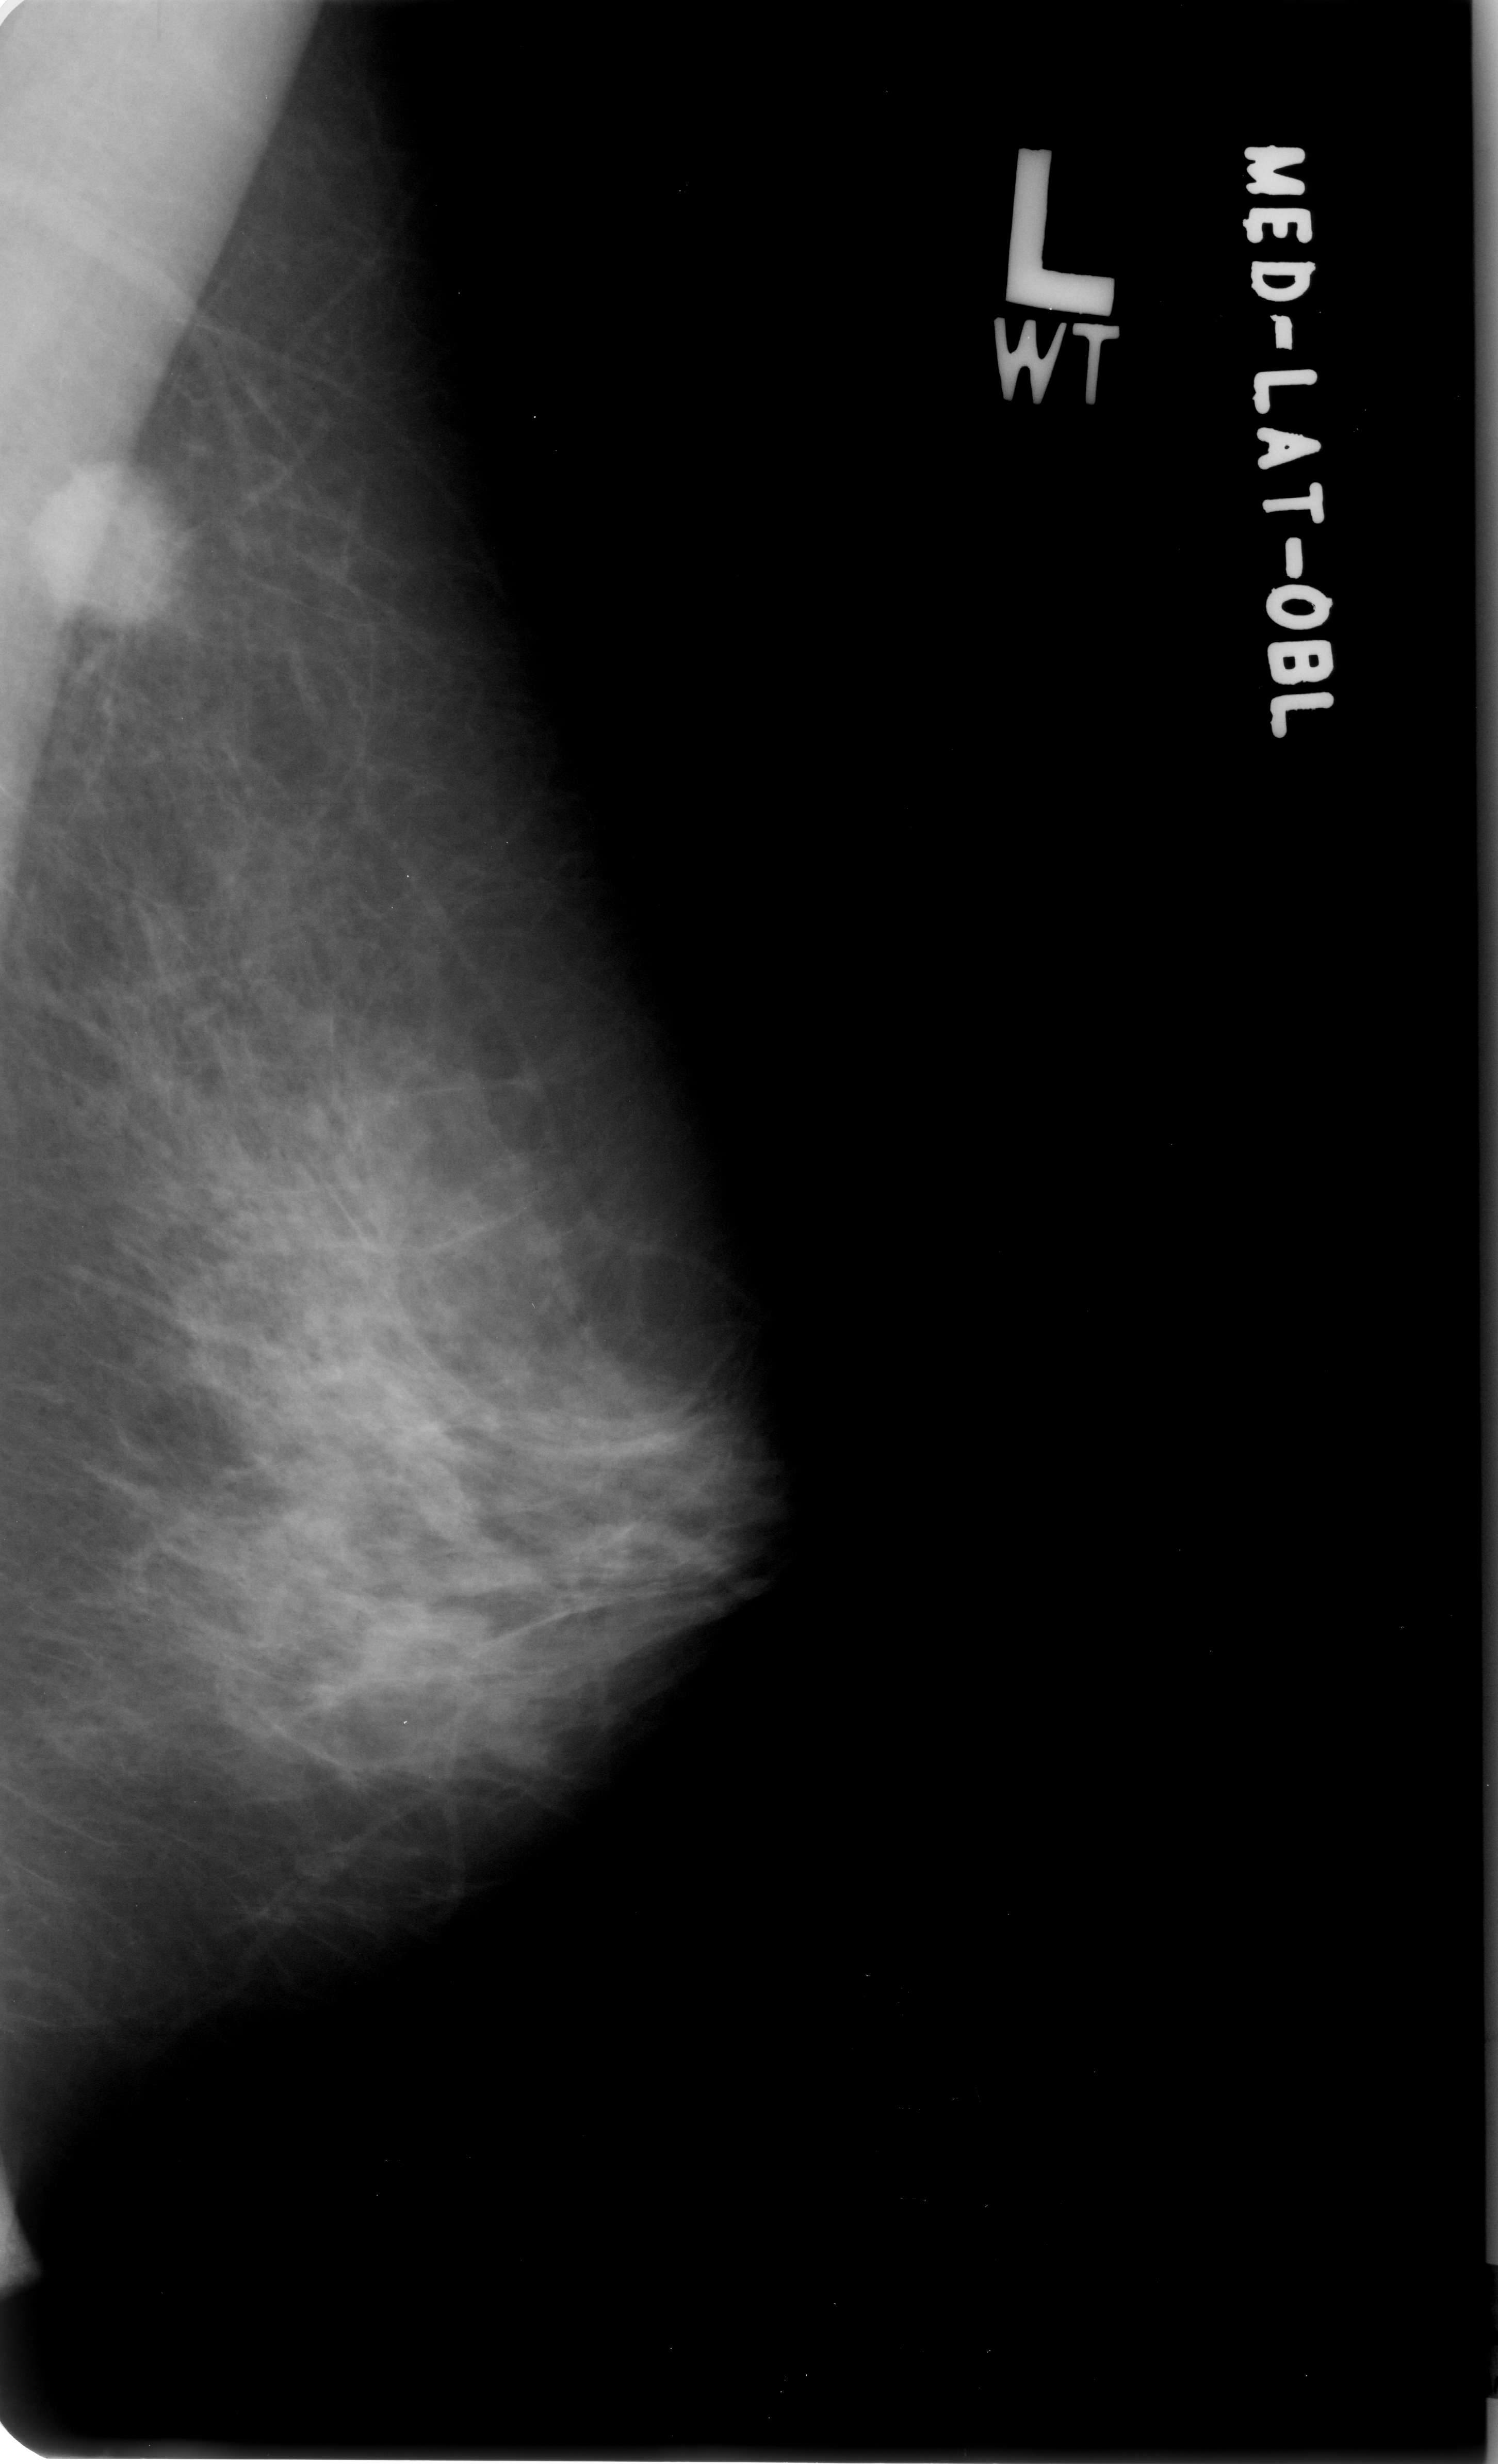
Digitized screen-film mammogram; left breast; mediolateral oblique (MLO) view; breast composition: heterogeneously dense (BI-RADS density category 3 of 4); 1498 × 2464 image matrix.
Marked abnormalities (boxes around the expert regions of interest):
- mass, shape round, margins ill defined; BI-RADS assessment category 4; subtlety rating 5 on a 1 (subtle) to 5 (obvious) scale; pathology (as recorded): malignant: box from (x=35, y=477) to (x=181, y=622) px